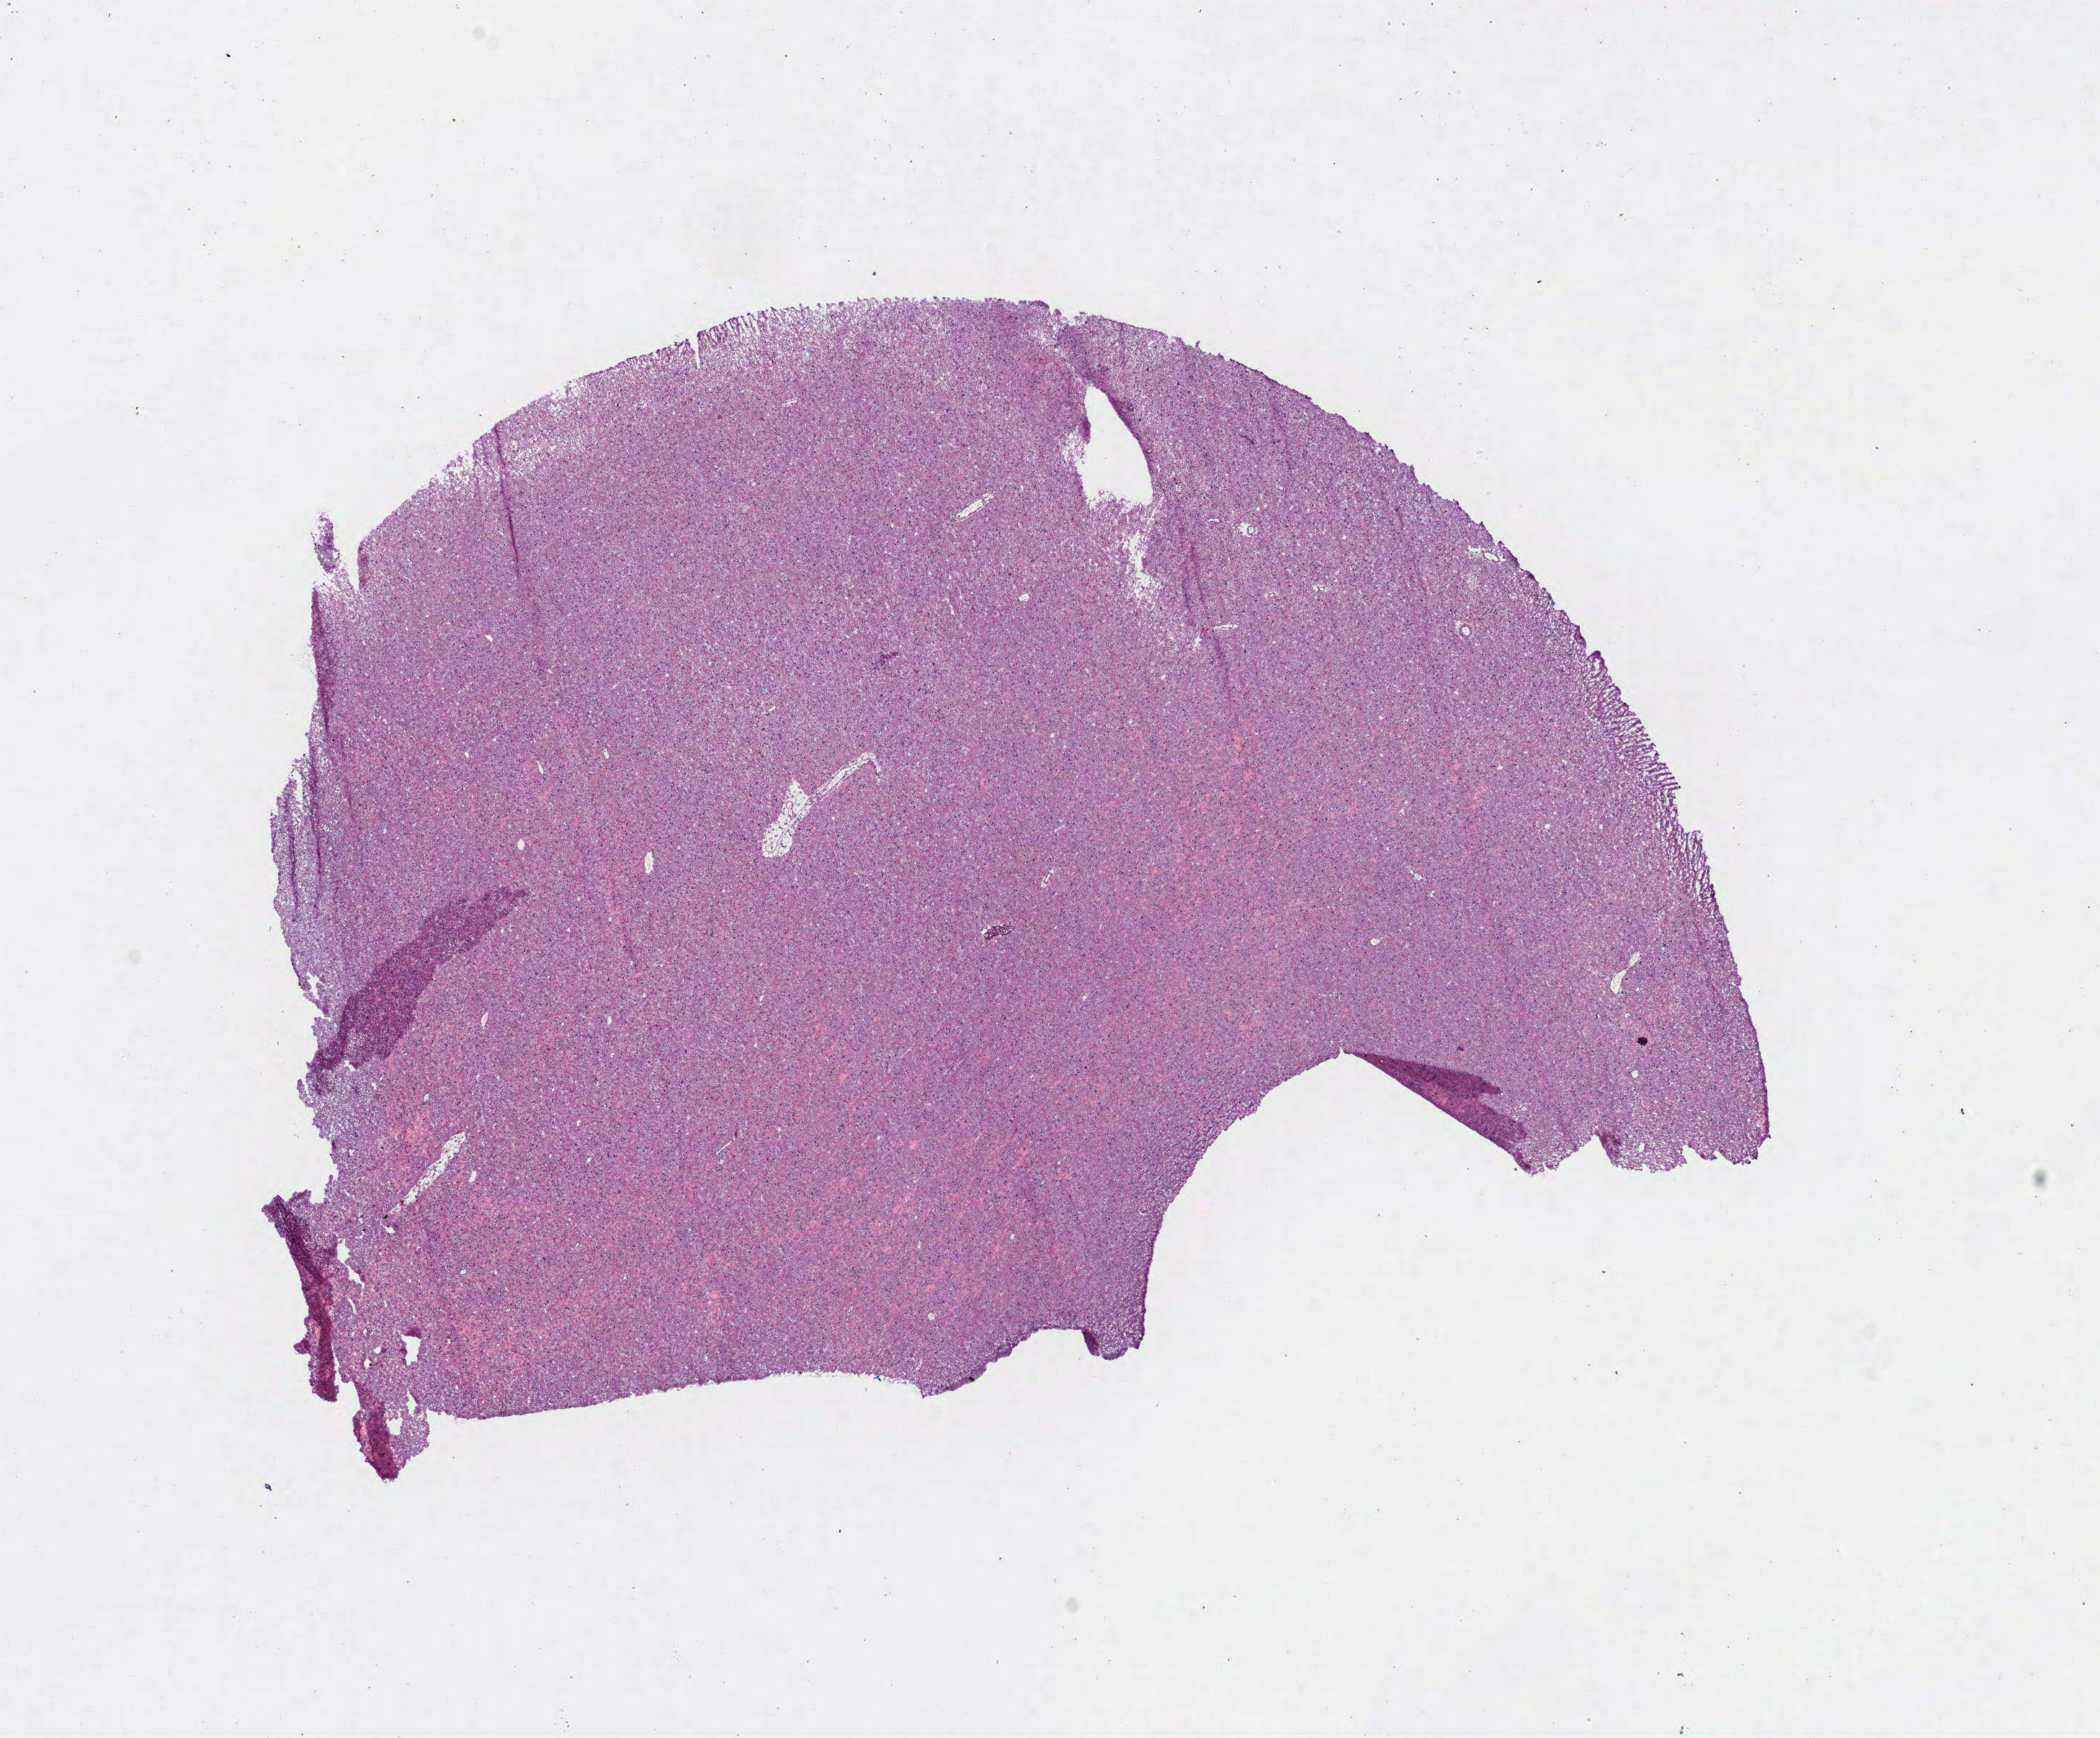
Digitized H&E tissue section (whole slide) — whole scanned area (about 11.5 x 9.5 mm) shown as a low-resolution overview. Frozen section. Brain, primary tumour sample. Patient: male, age at initial diagnosis 23 years. Histologic grade: G3 (poorly differentiated). Pathologist review of this section (percent, as recorded): tumour cells 50%, tumour nuclei 20%, normal cells 50%, stromal cells 0%, necrosis 0%.
• laterality: right
• histologic diagnosis: Astrocytoma, anaplastic (cerebrum)